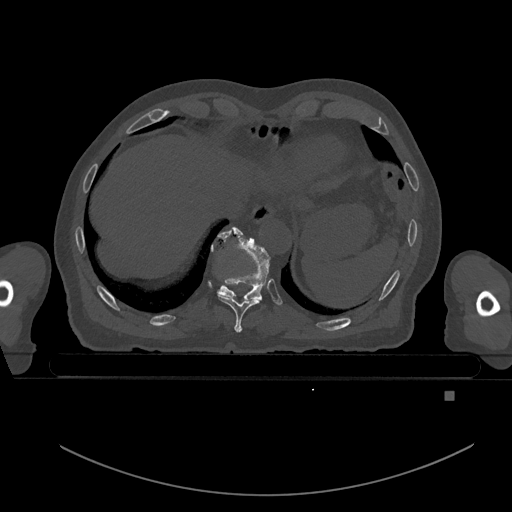
CT including the spine, one axial slice; position 120 of 969 along the scan axis; bone window (W 1800 / L 400 HU); 0.5 mm slice thickness; 512 × 512 image matrix, field of view 456 × 456 mm. Patient: male, 82 years. From the clinical record (not read from this slice): primary cancer: prostate.
Outlined on this slice (semi-automatic segmentation, software-assisted and operator-edited):
- T10 vertebra: bounding box (x1, y1, x2, y2) in pixels: (211, 226, 270, 300)
- T9 vertebra: (217, 230, 262, 333)